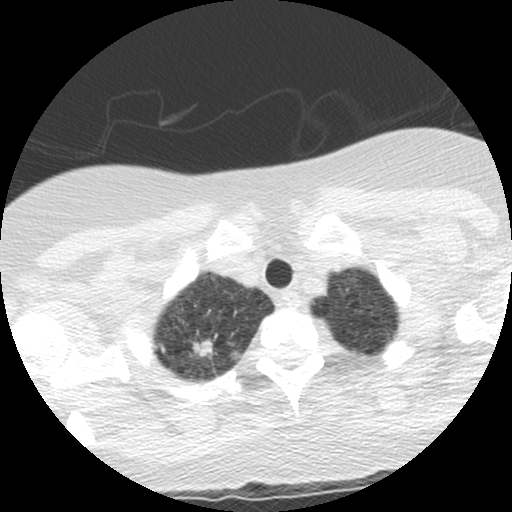
Low-dose screening chest CT, one axial slice; position 118 of 130 along the scan axis; reconstruction kernel STANDARD; 120 kVp; lung window (W 1500 / L -600 HU); 2.5 mm slice thickness; 512 × 512 image matrix, field of view 290 × 290 mm.
Structures marked on this image (outlined manually by an expert reader):
- lesion 1 (tumor, upper lobe of right lung): bounding box <192,340,212,357> (left, top, right, bottom; pixels)